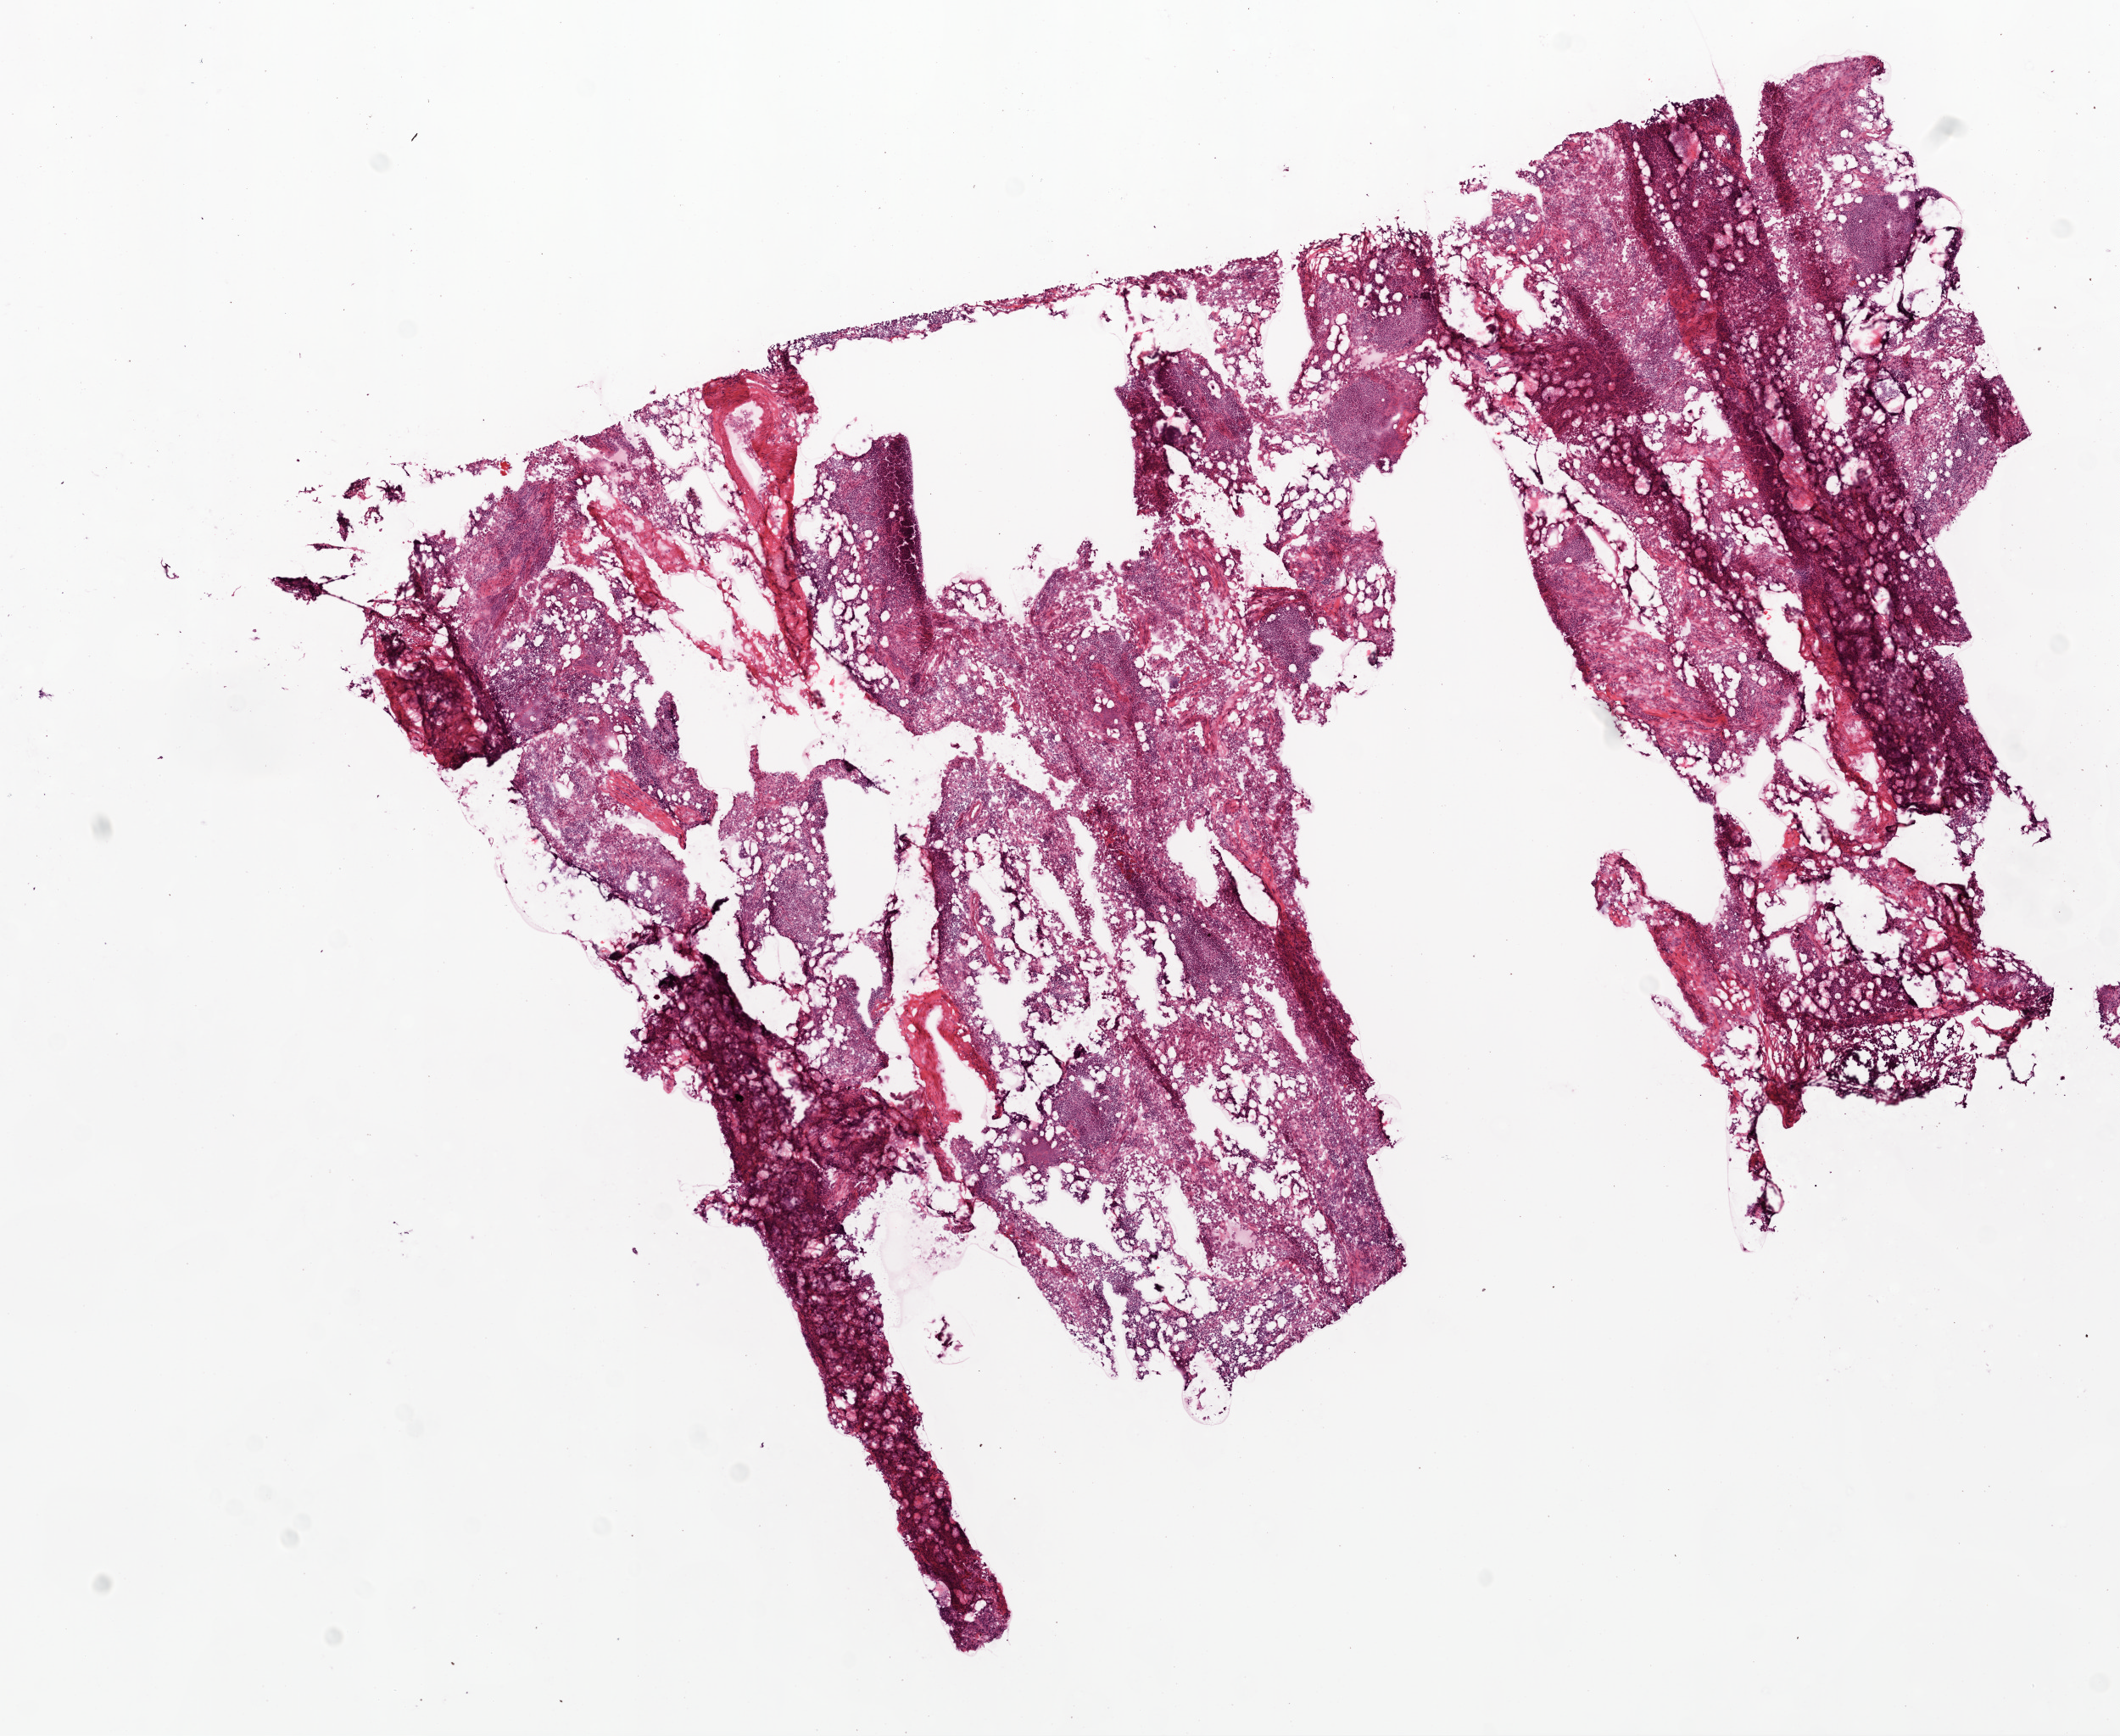
Digitized Hematoxylin and eosin (H&E) stained tissue section (whole slide), shown as a low-resolution overview of the whole scanned area (about 10.0 x 8.2 mm, from a 20x scan). Frozen section from the top of the tissue portion. Sample: solid tissue normal (non-tumour tissue), ovary. Female patient; age at initial diagnosis 57 years.
This section: solid tissue normal (non-tumour) sample from the same patient. Patient diagnosis: Serous cystadenocarcinoma, NOS.